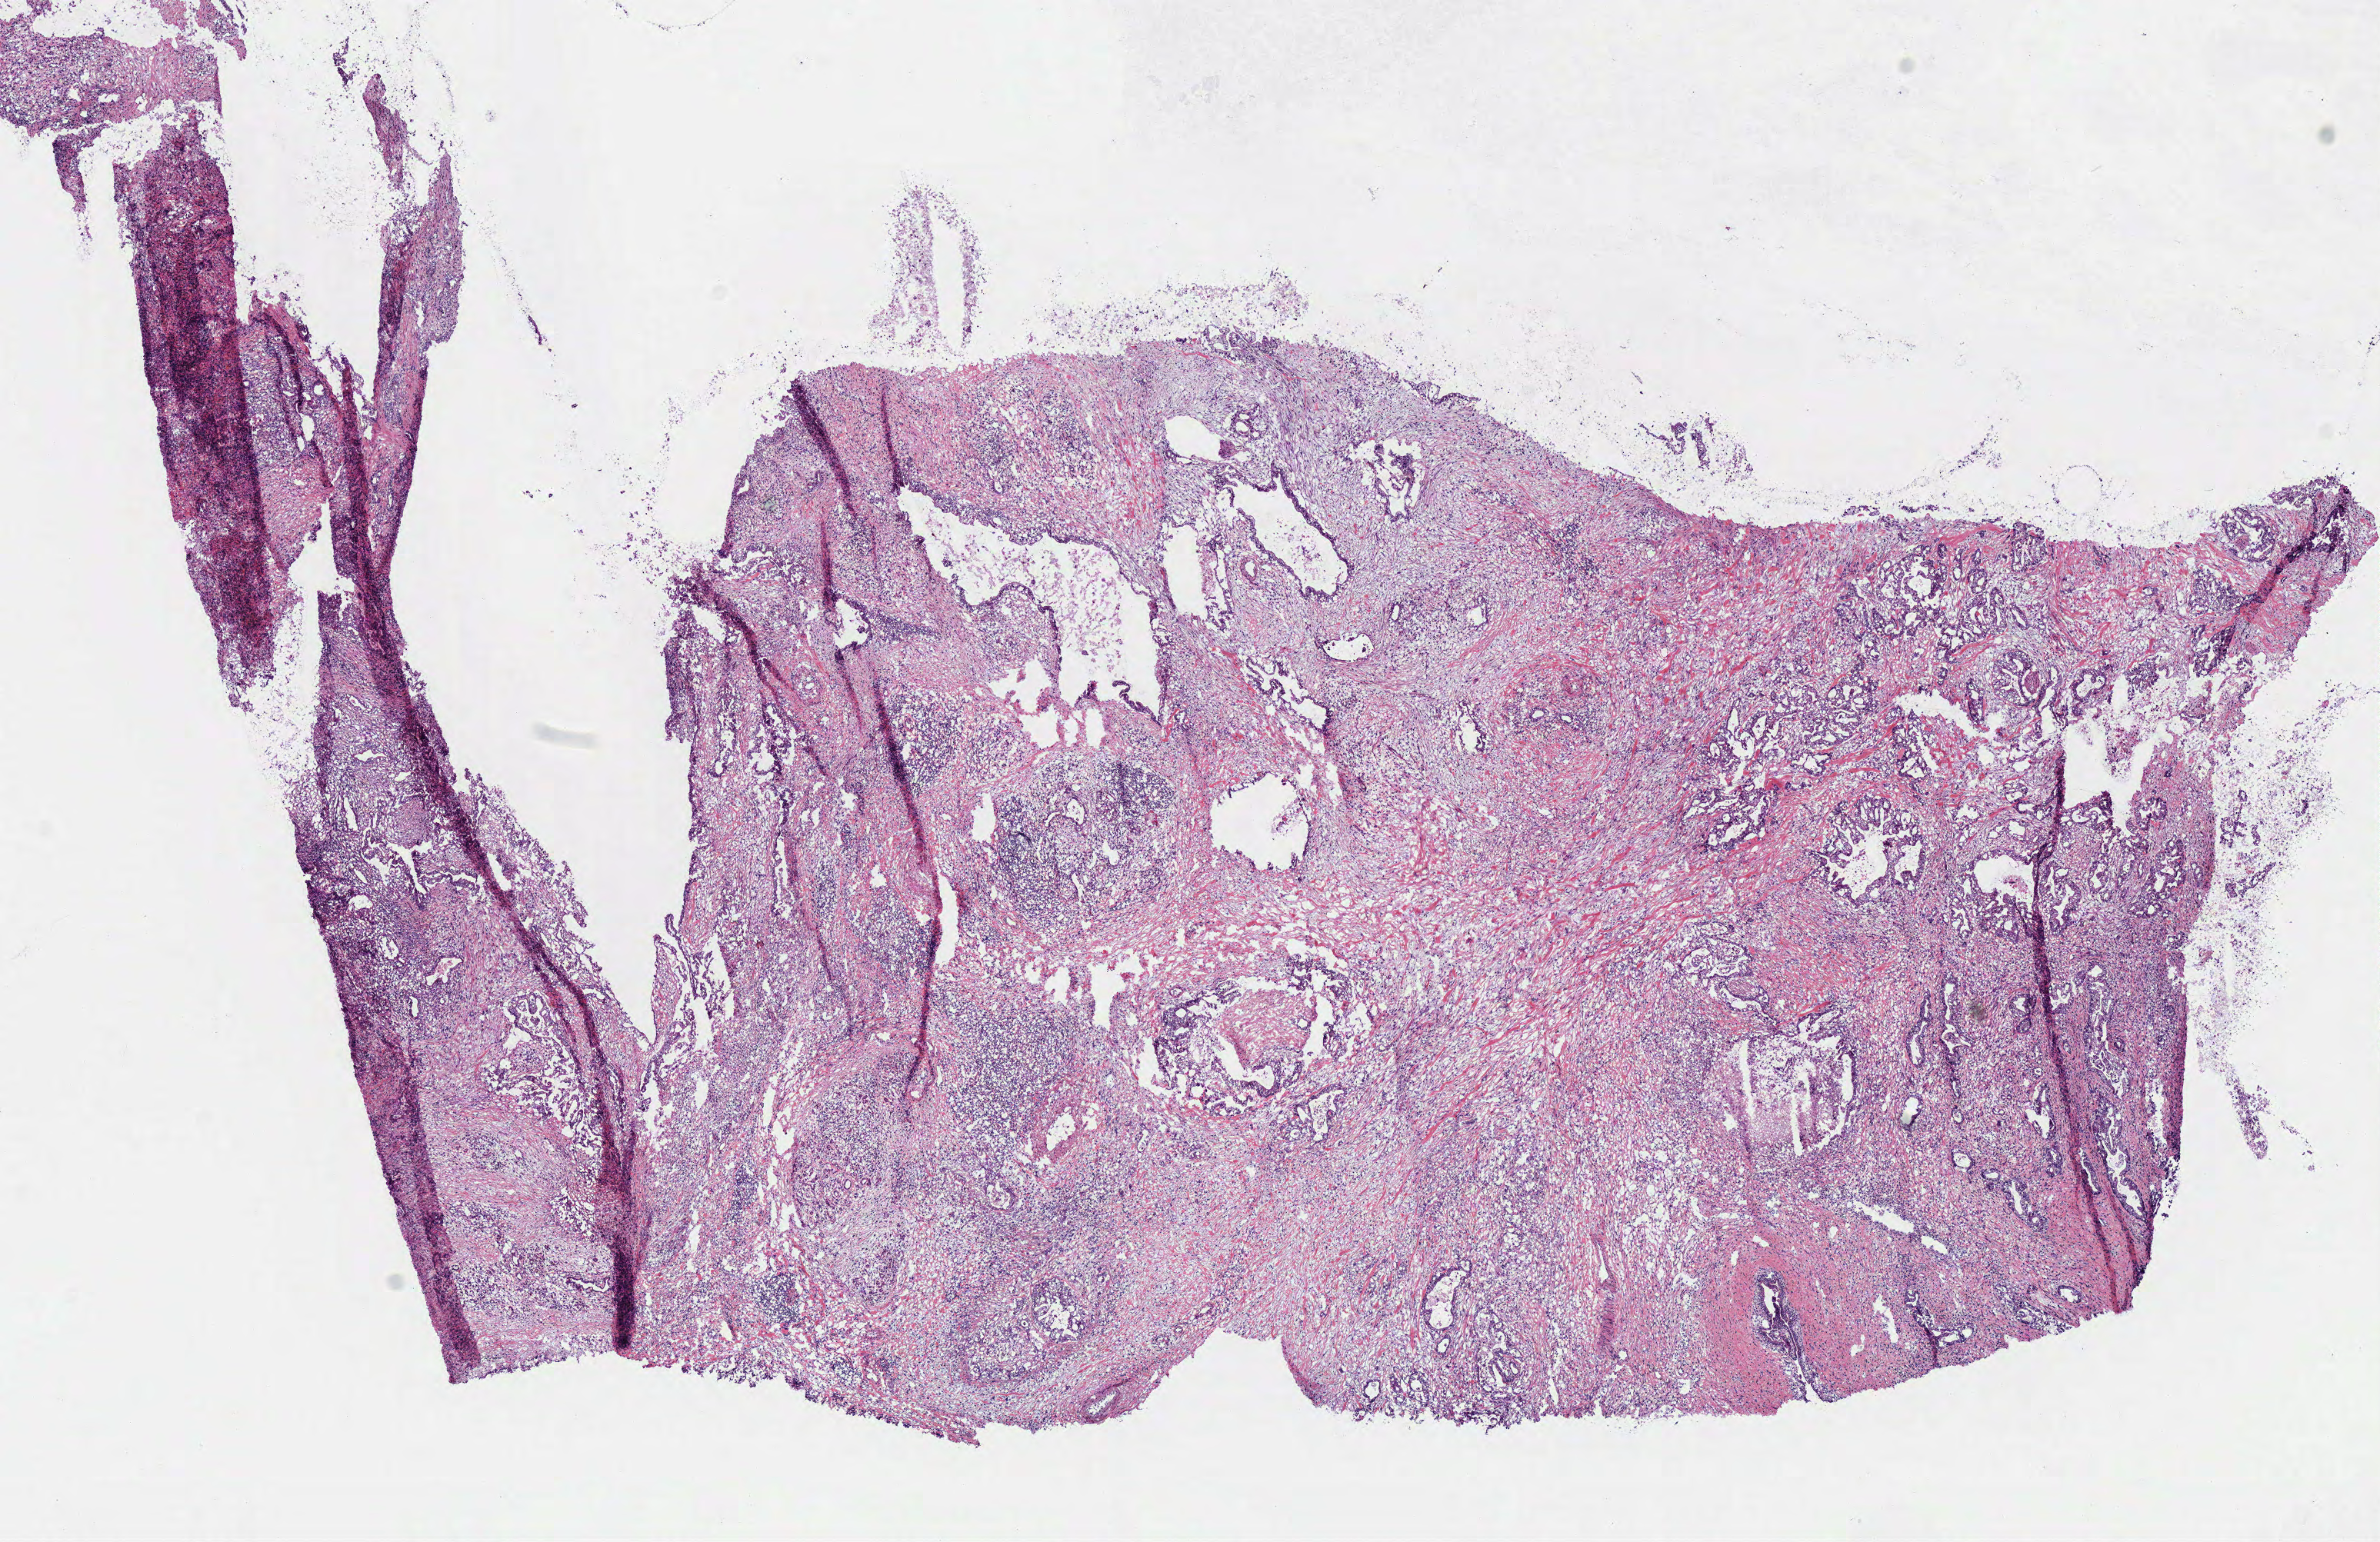
H&E whole-slide image — whole scanned area (about 12.2 x 7.9 mm) shown as a low-resolution overview, frozen section from the top of the tissue portion, pancreas, primary tumour sample. Female, age 59 years at initial diagnosis. Histologic grade: G3 (poorly differentiated). Slide review estimates, as recorded: tumour cells 40%, tumour nuclei 60%, normal cells 0%, stromal cells 57%, necrosis 3%. Inflammatory infiltration, as recorded: lymphocyte infiltration 20%.
Diagnosis: Infiltrating duct carcinoma, NOS (head of pancreas). Lymph nodes positive (case pathology): 9 of 11 examined. AJCC pathologic stage: IIB (6th edition).